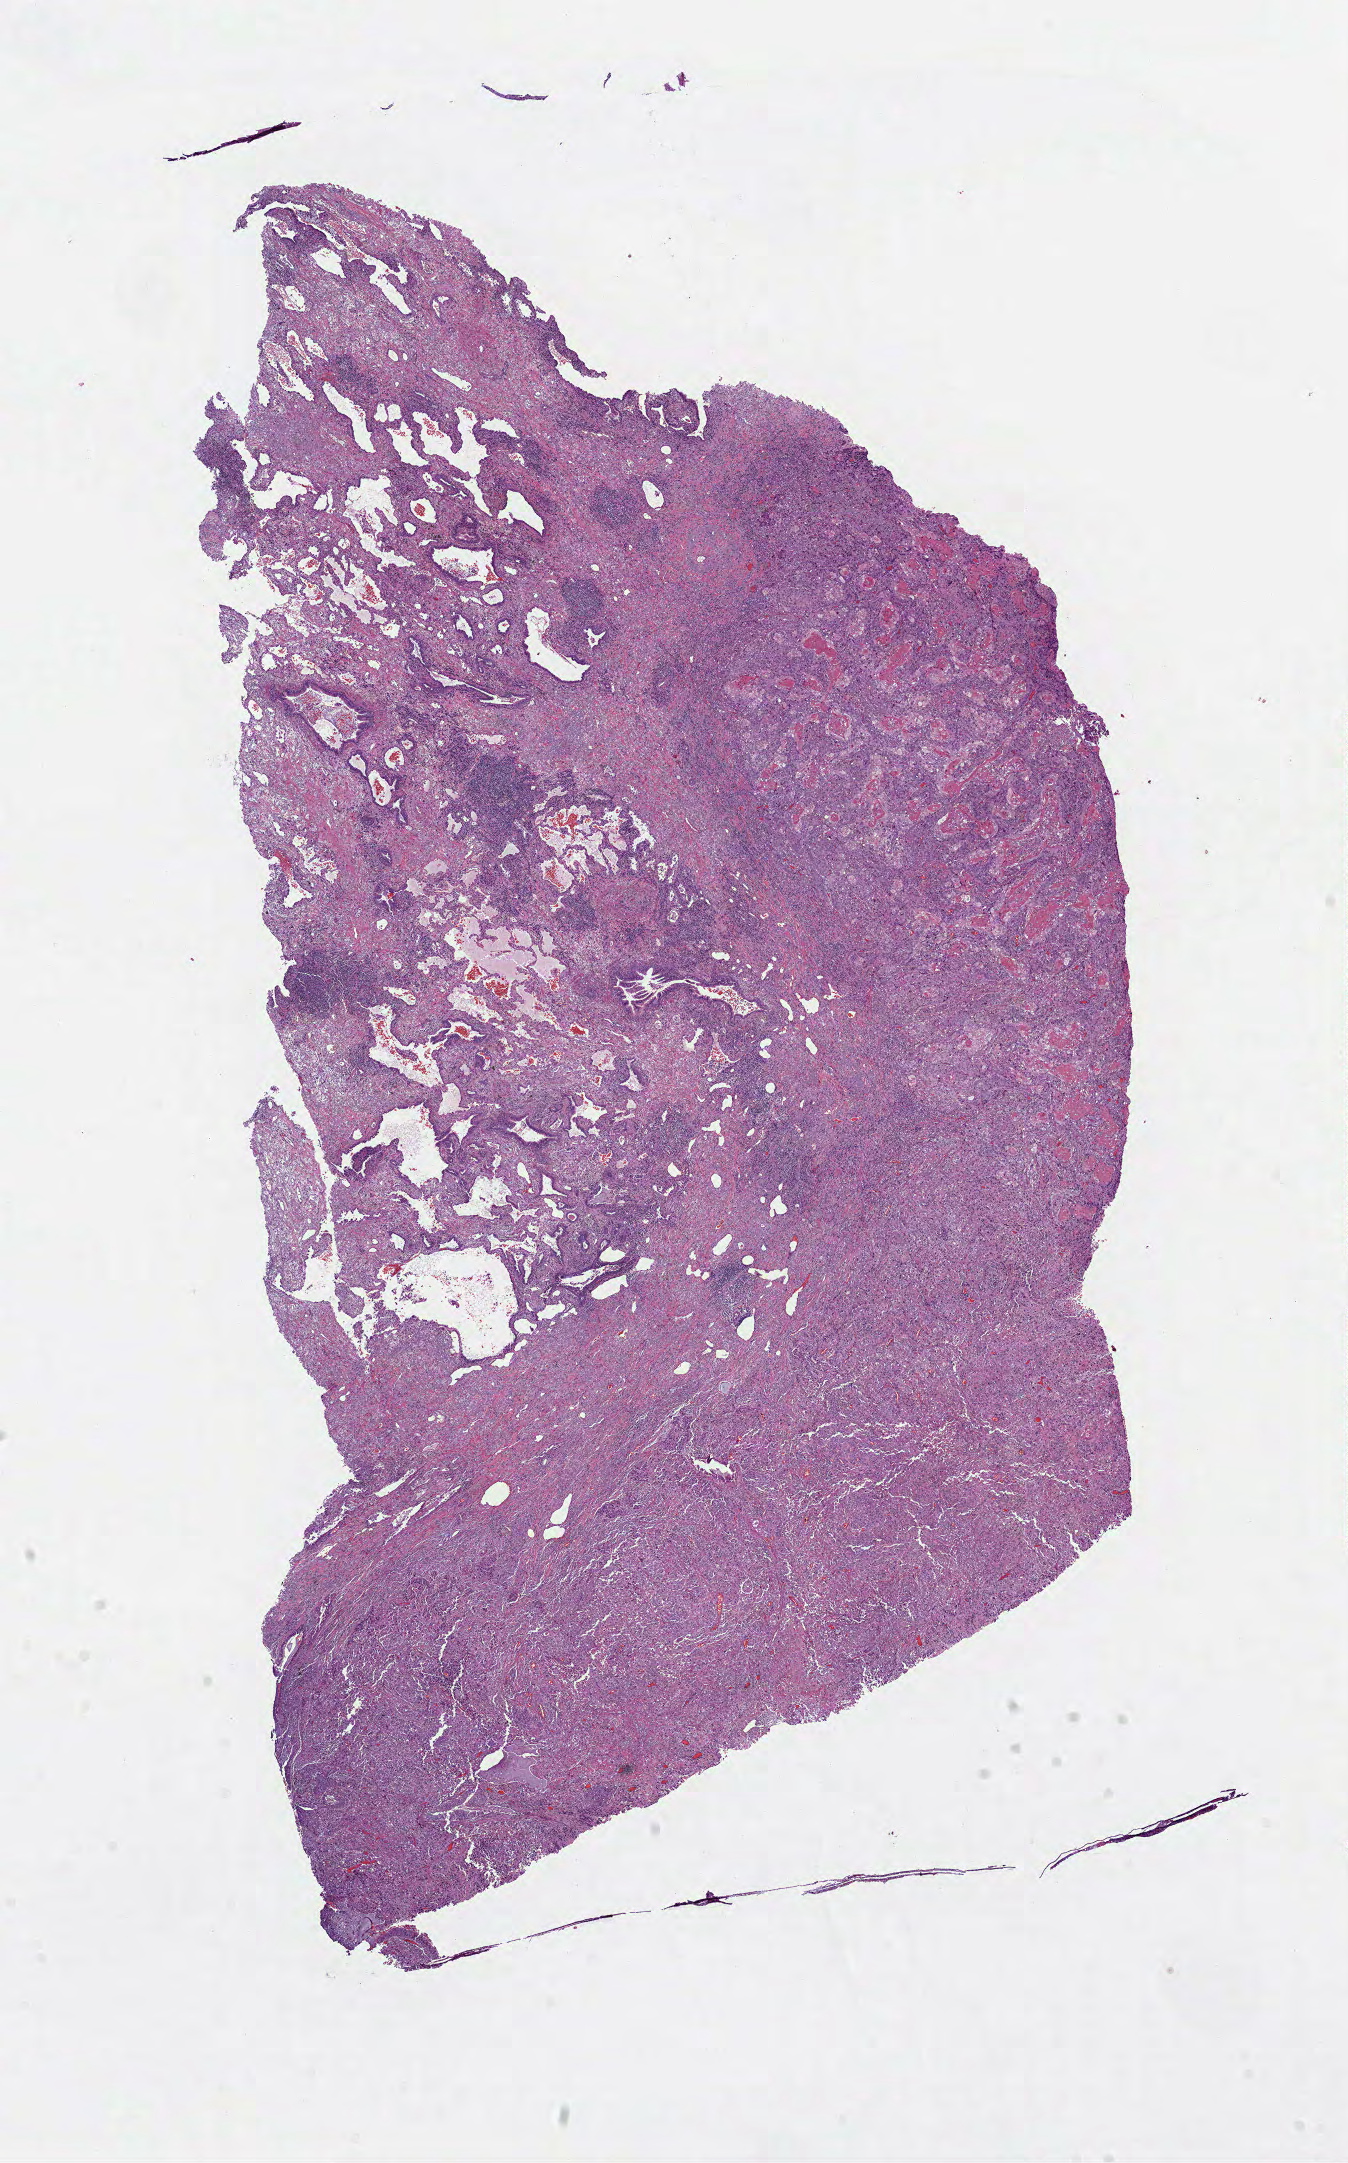
Whole-slide histology image, H&E, shown as a low-resolution overview of the whole scanned area (about 10.9 x 17.5 mm, from a 40x scan); formalin-fixed paraffin-embedded (FFPE) diagnostic section; lung, primary tumour sample. Patient: male, age at initial diagnosis 78 years.
- histologic diagnosis: Squamous cell carcinoma, NOS (upper lobe, lung)
- laterality: left
- AJCC pathologic stage: IIA (7th edition)